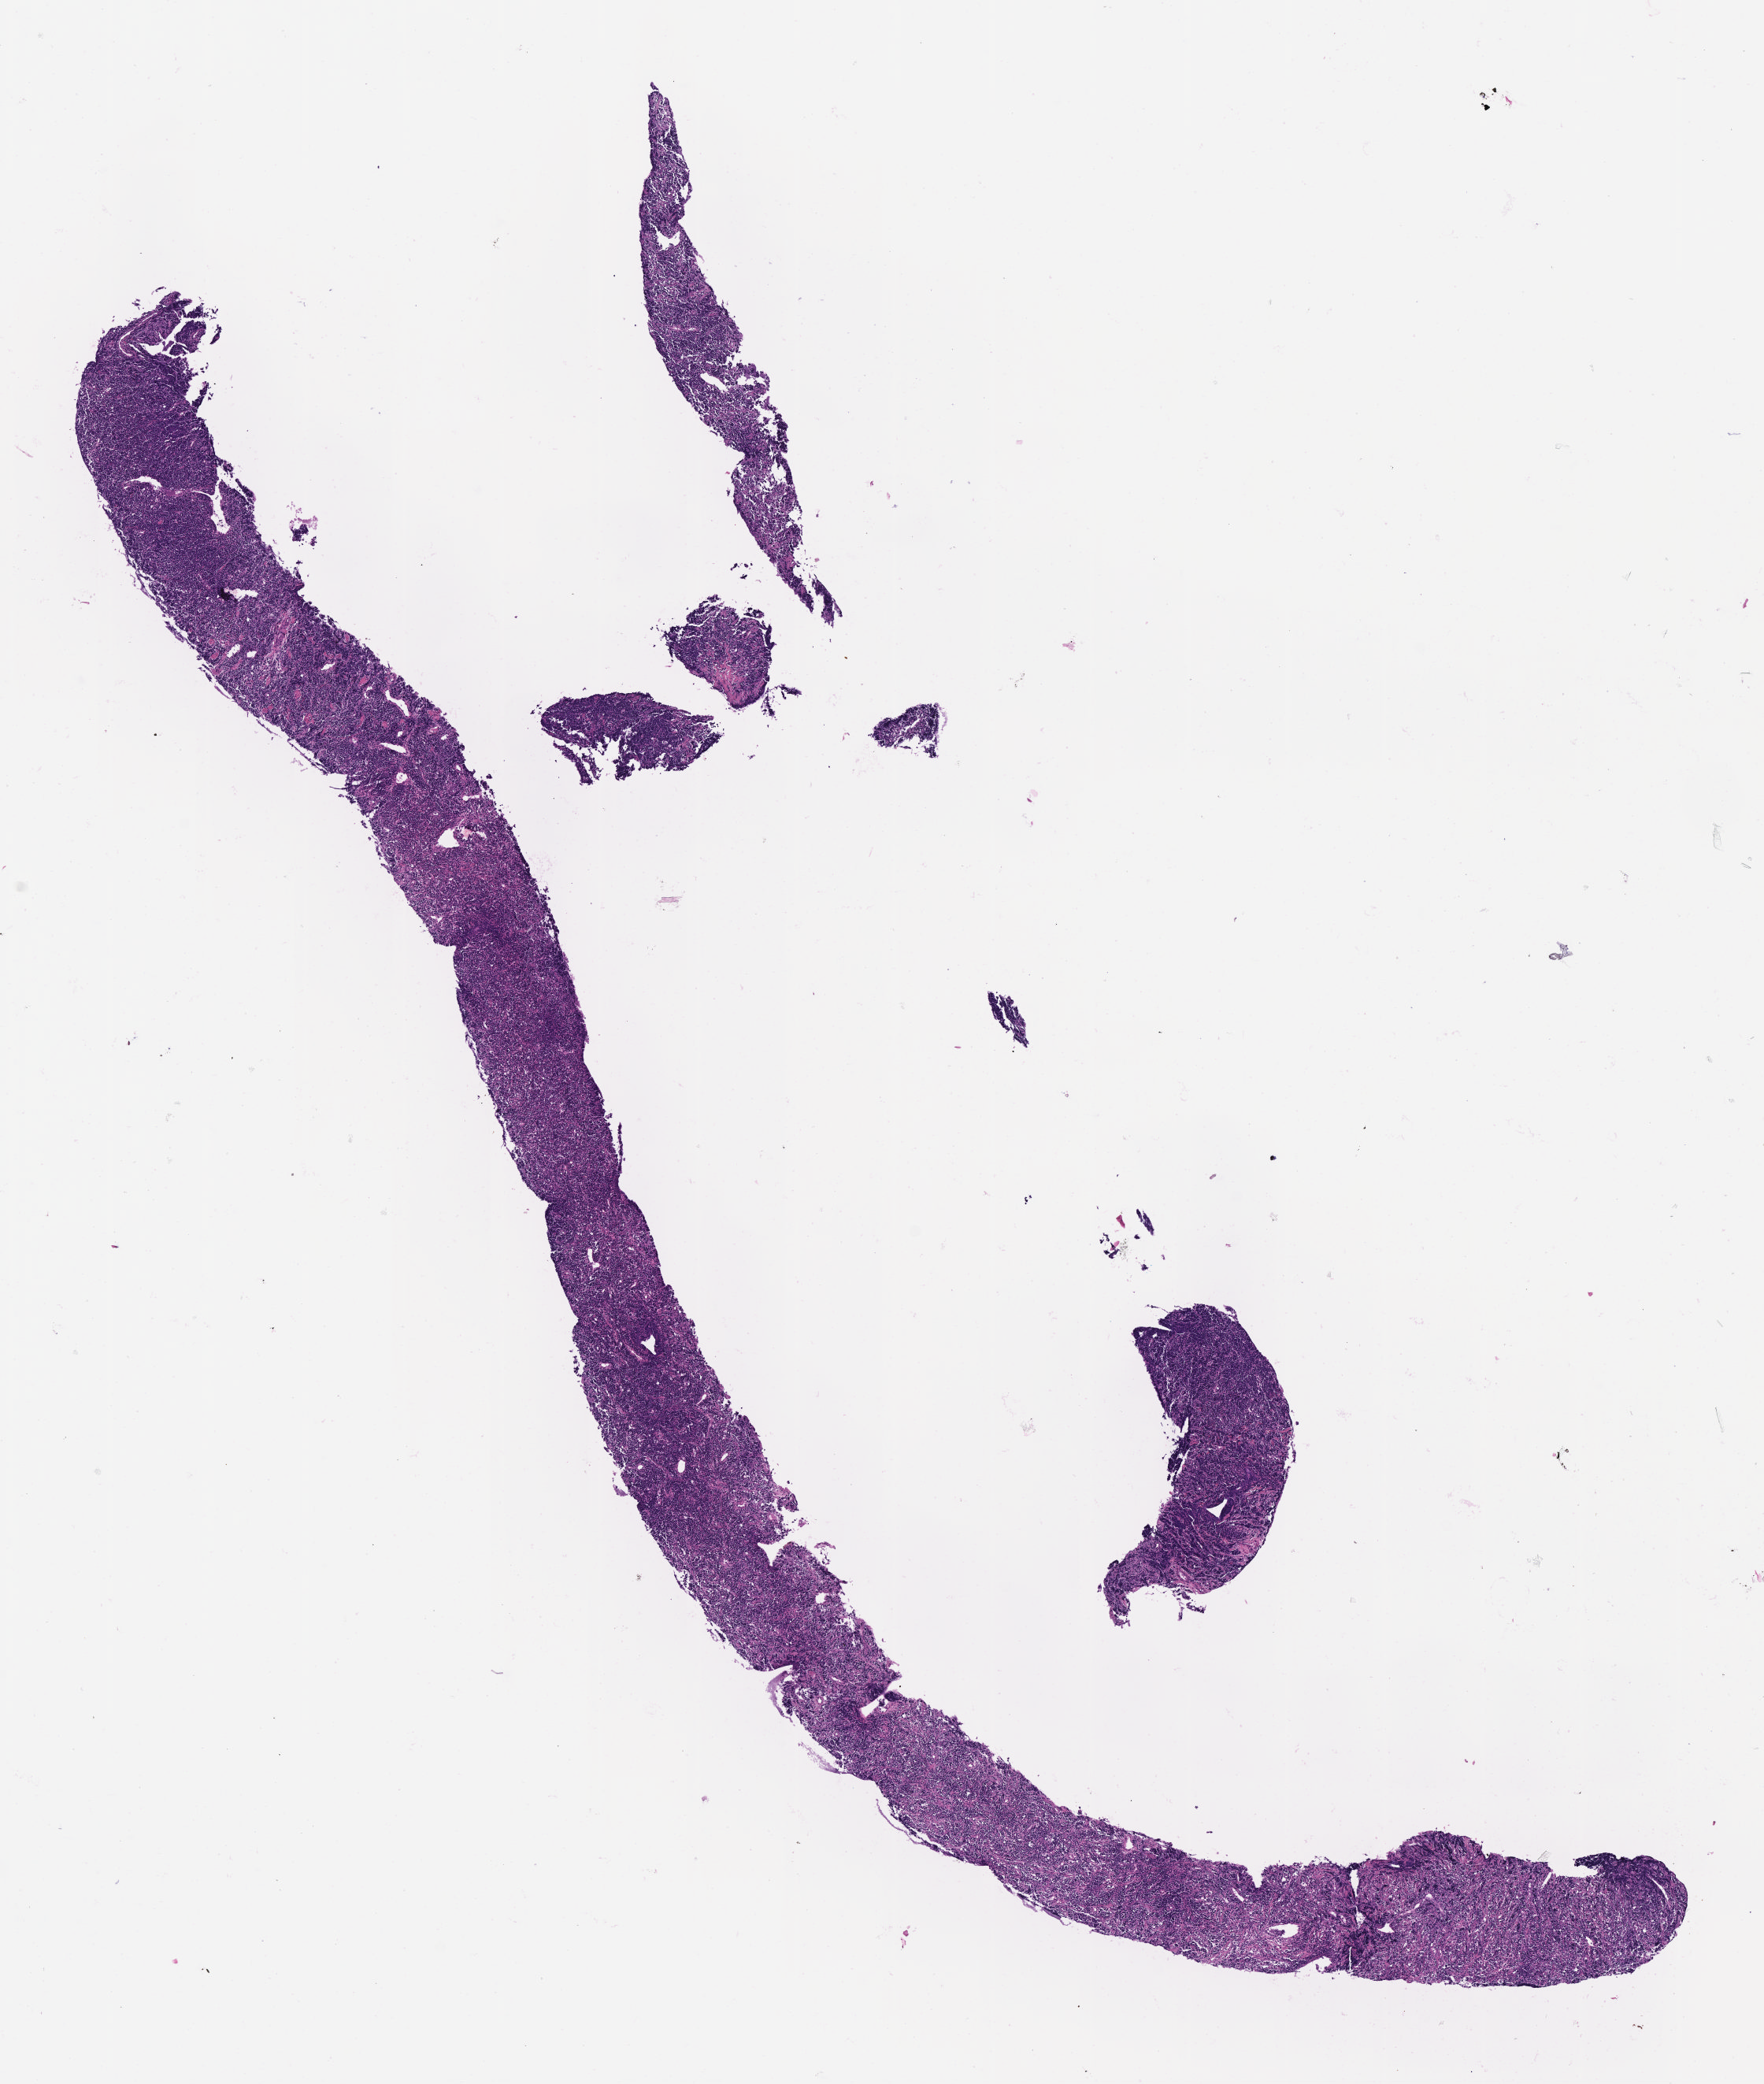
Digitized hematoxylin and eosin (H&E)-stained section, low-resolution overview of the scanned area, about 9.1 x 10.7 mm, tumor tissue, anatomic site: ovary. Female, age 9 years at initial diagnosis.
- diagnosis: Burkitt lymphoma, NOS